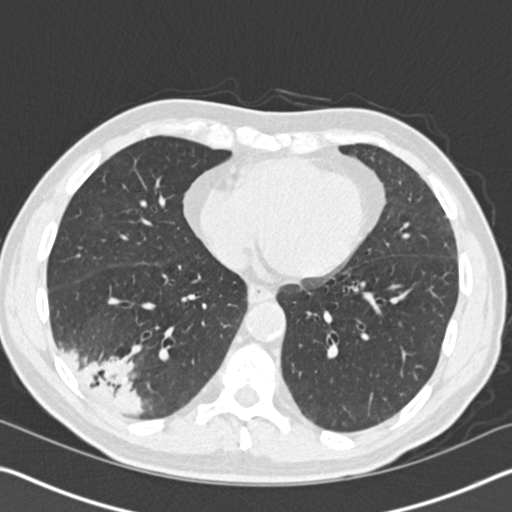
Chest CT (low-dose screening protocol), one axial image, baseline screening round, lung window (W 1500 / L -600 HU), 2 mm slice thickness, slice 102 of 161 in the series. Male, age 61 years at enrolment.
Expert reader's lesion annotation, bounding box [x1, y1, x2, y2] px = [39, 314, 153, 422]. Reader record for this screening exam (exam-level; its link to the box is not recorded): non-calcified nodule or mass ≥4 mm, right lower lobe, 52 × 36 mm, spiculated (stellate) margins, soft tissue attenuation. Participant outcome: lung cancer diagnosed 392 days after this screen — bronchiolo-alveolar adenocarcinoma, NOS, right lower lobe, moderately differentiated (G2), stage IIIB (AJCC 6th edition), 90 mm at pathology.